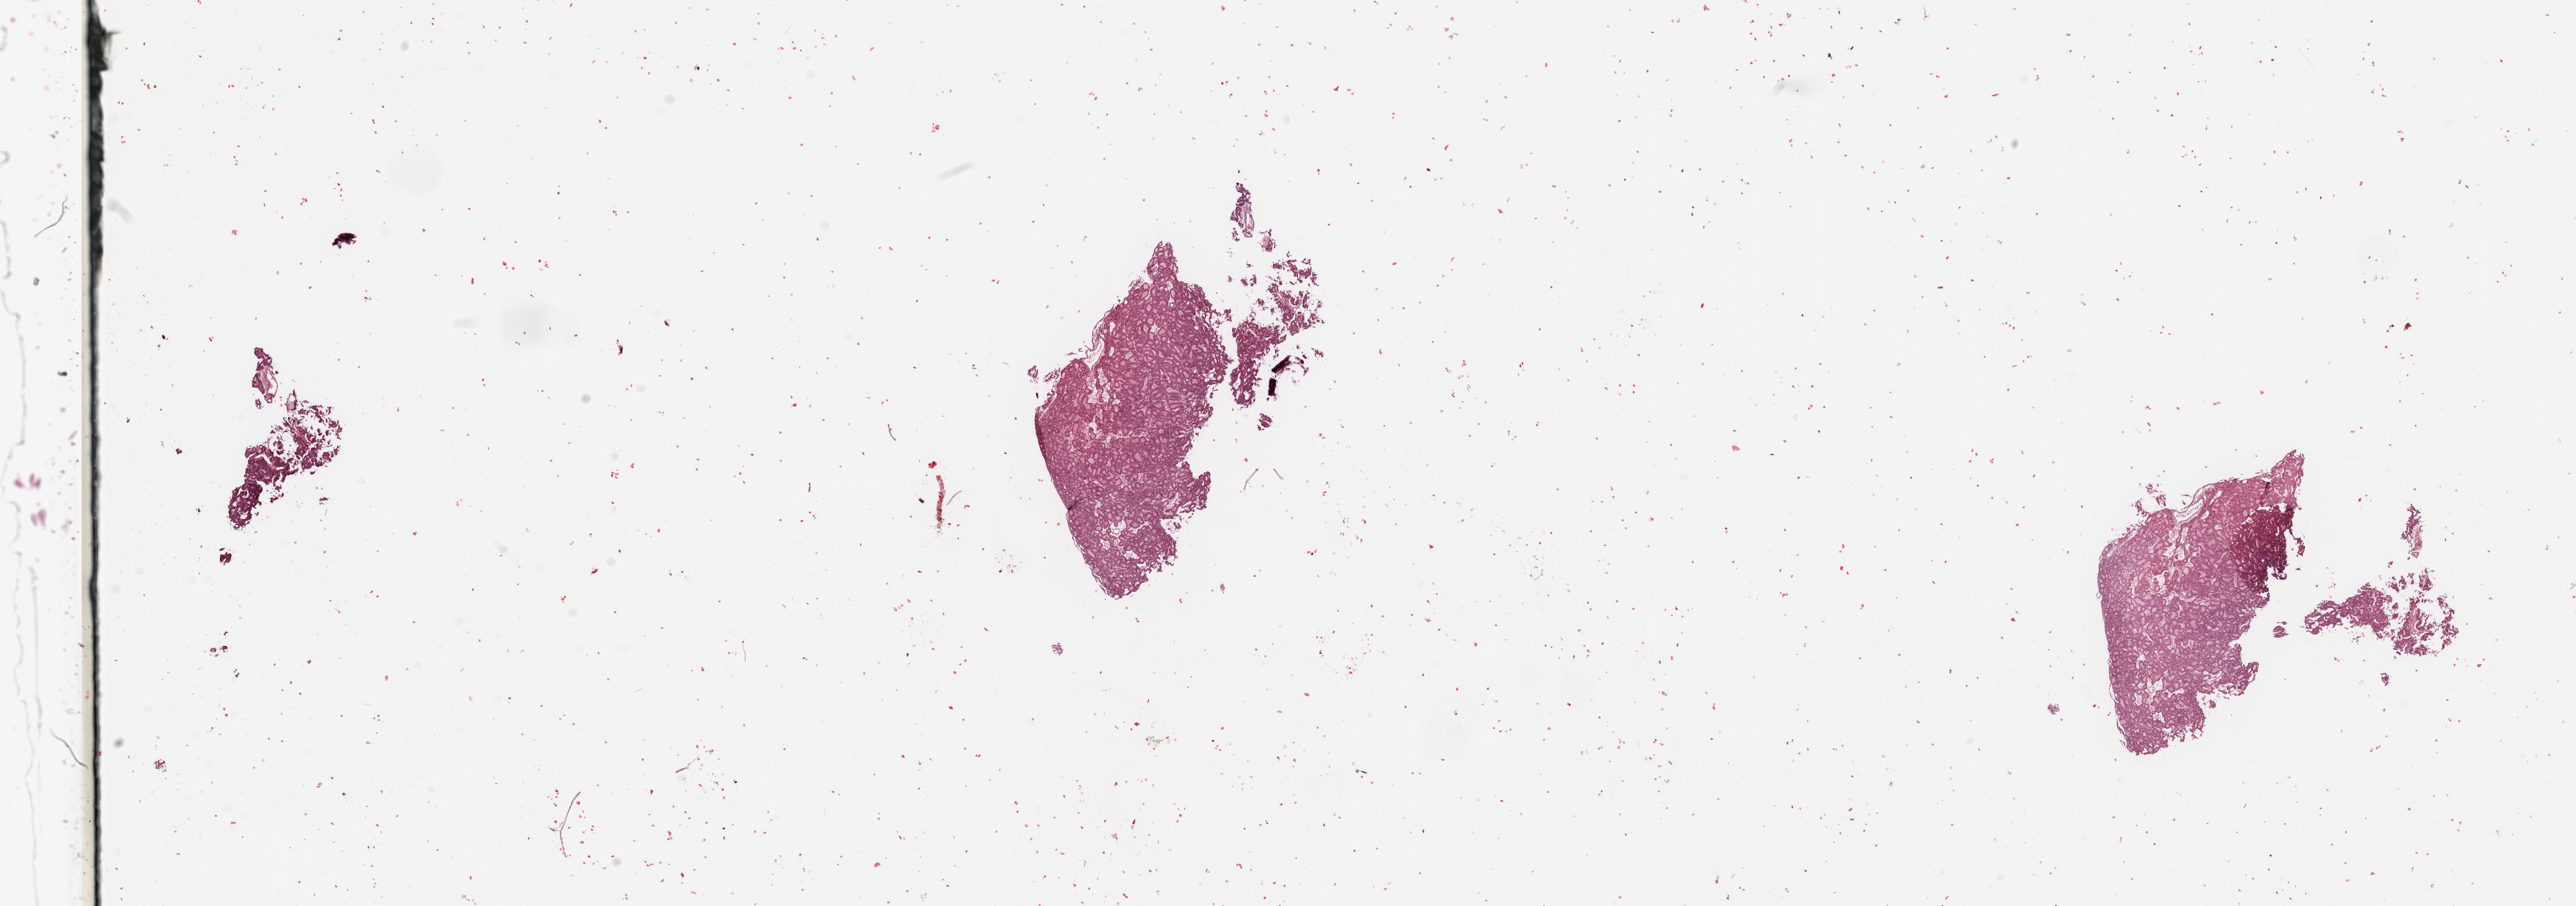
H&E-stained whole-slide image, low-resolution overview of the scanned area, about 31.5 x 11.1 mm. Uterus, tumour tissue. Patient: female, age 71 years. Histologic grade: G2 (moderately differentiated).
AJCC pathologic stage: I. Primary tumour site (as recorded): anterior endometrium. Histologic diagnosis: Endometrioid adenocarcinoma, NOS.